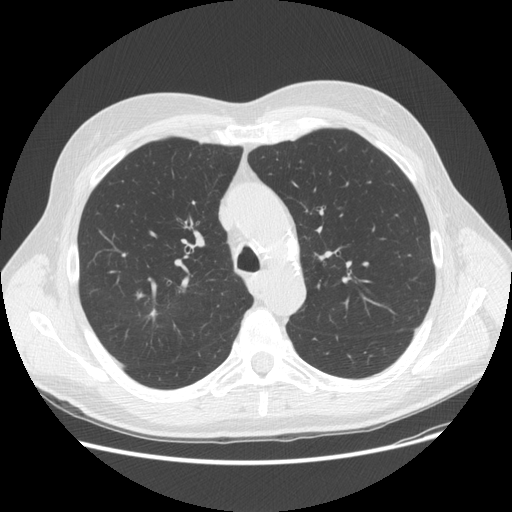
Low-dose screening chest CT, one axial slice. Position 110 of 156 along the scan axis. Reconstruction kernel STANDARD. 120 kVp. Lung window (W 1500 / L -600 HU). 2.5 mm slice thickness. 512 × 512 image matrix, field of view 380 × 380 mm.
Annotated regions visible in this slice (outlined manually by an expert reader):
- lesion 1 (tumor, upper lobe of right lung): box from (x=149, y=309) to (x=175, y=326) px